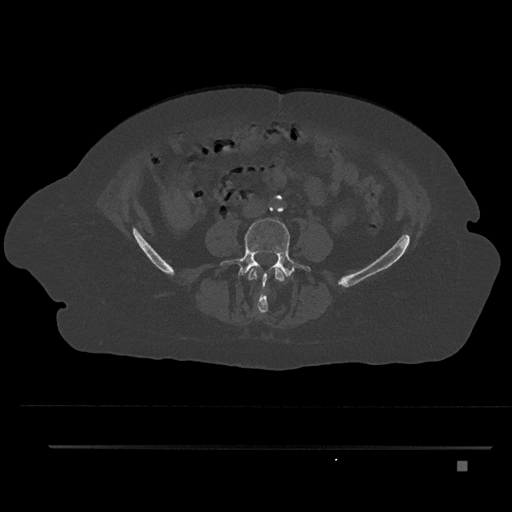
CT including the spine, one axial slice. Position 91 of 797 along the scan axis. Bone window (W 1800 / L 400 HU). 512 × 512 image matrix, field of view 437 × 437 mm. Female patient, age 76 years. From the clinical record (not read from this slice): primary cancer: lung.
Structures marked on this image (semi-automatic segmentation, software-assisted and operator-edited):
- L3 vertebra: bounding box [x1, y1, x2, y2] px = [248, 267, 285, 315]
- L4 vertebra: [220, 218, 311, 300]